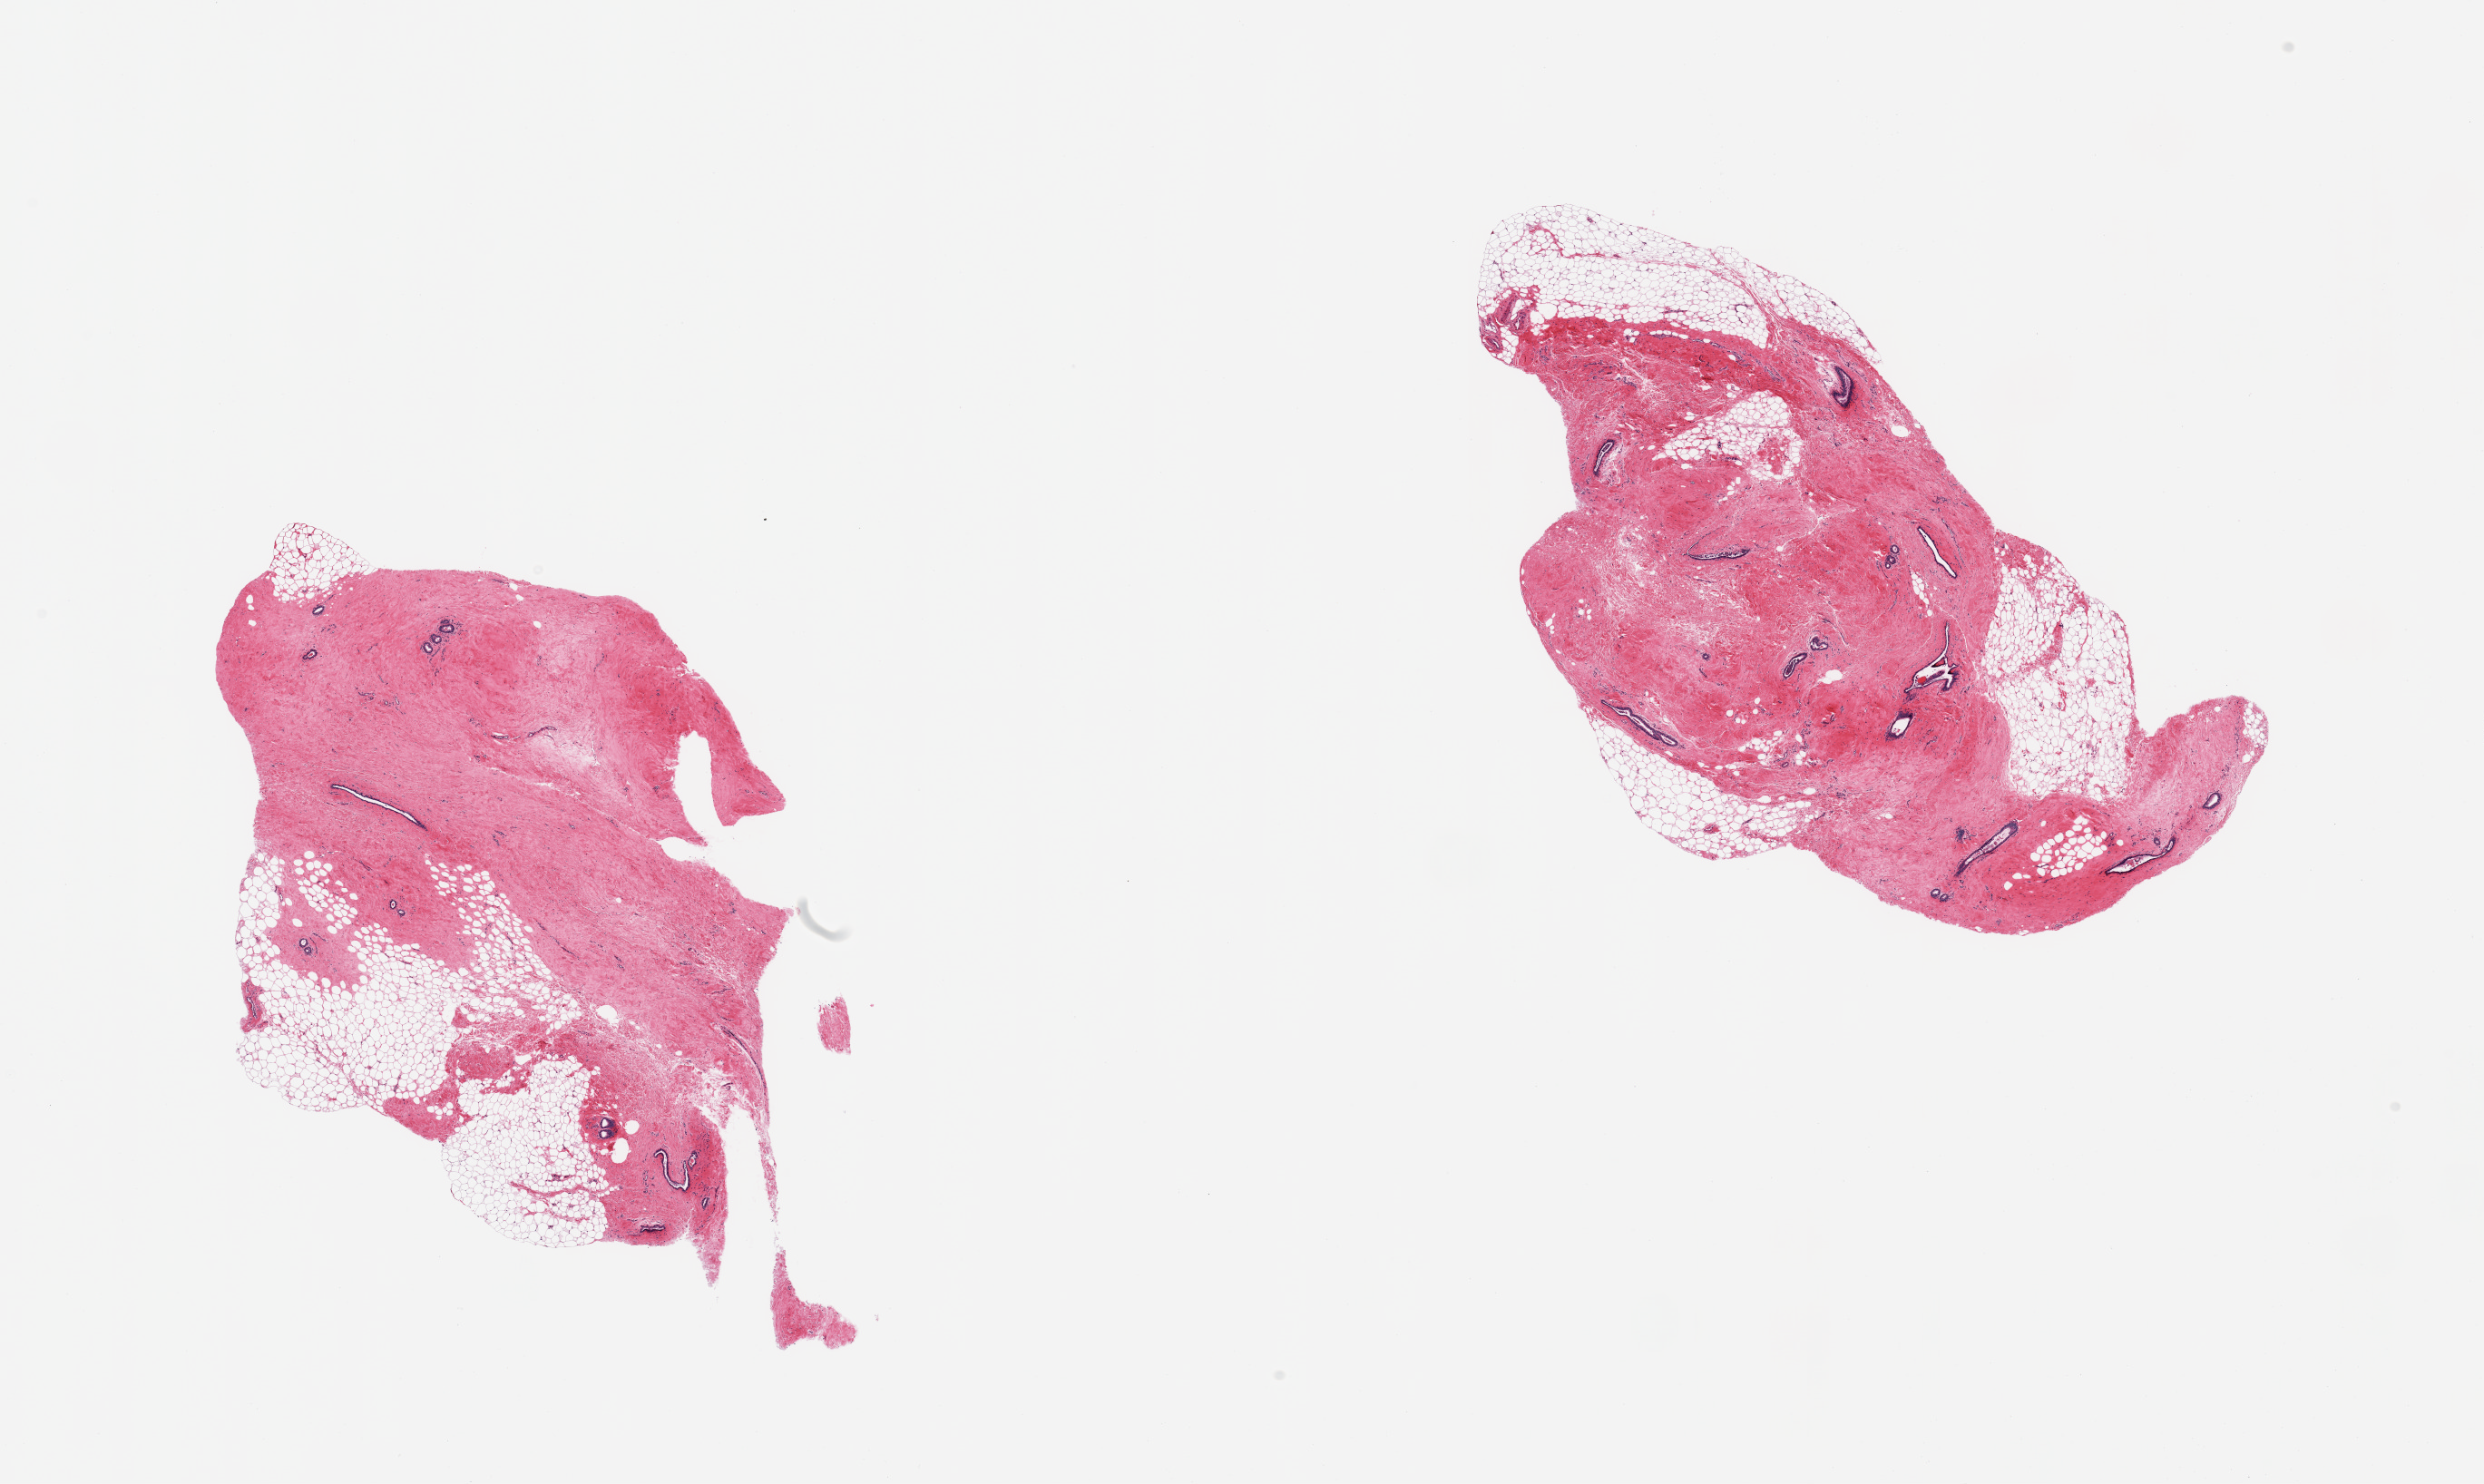
Whole-slide image, hematoxylin and eosin (H&E) stain, brightfield — a low-resolution overview of the entire scanned area, about 21.7 x 12.9 mm, PAXgene-fixed, paraffin-embedded tissue, section of breast (target tissue), tissue donor sample. Donor sex: male.
Review note (as recorded): 2 pieces; gynecomastoid ductal and stromal hyperplasia with 40% and 30% fat.